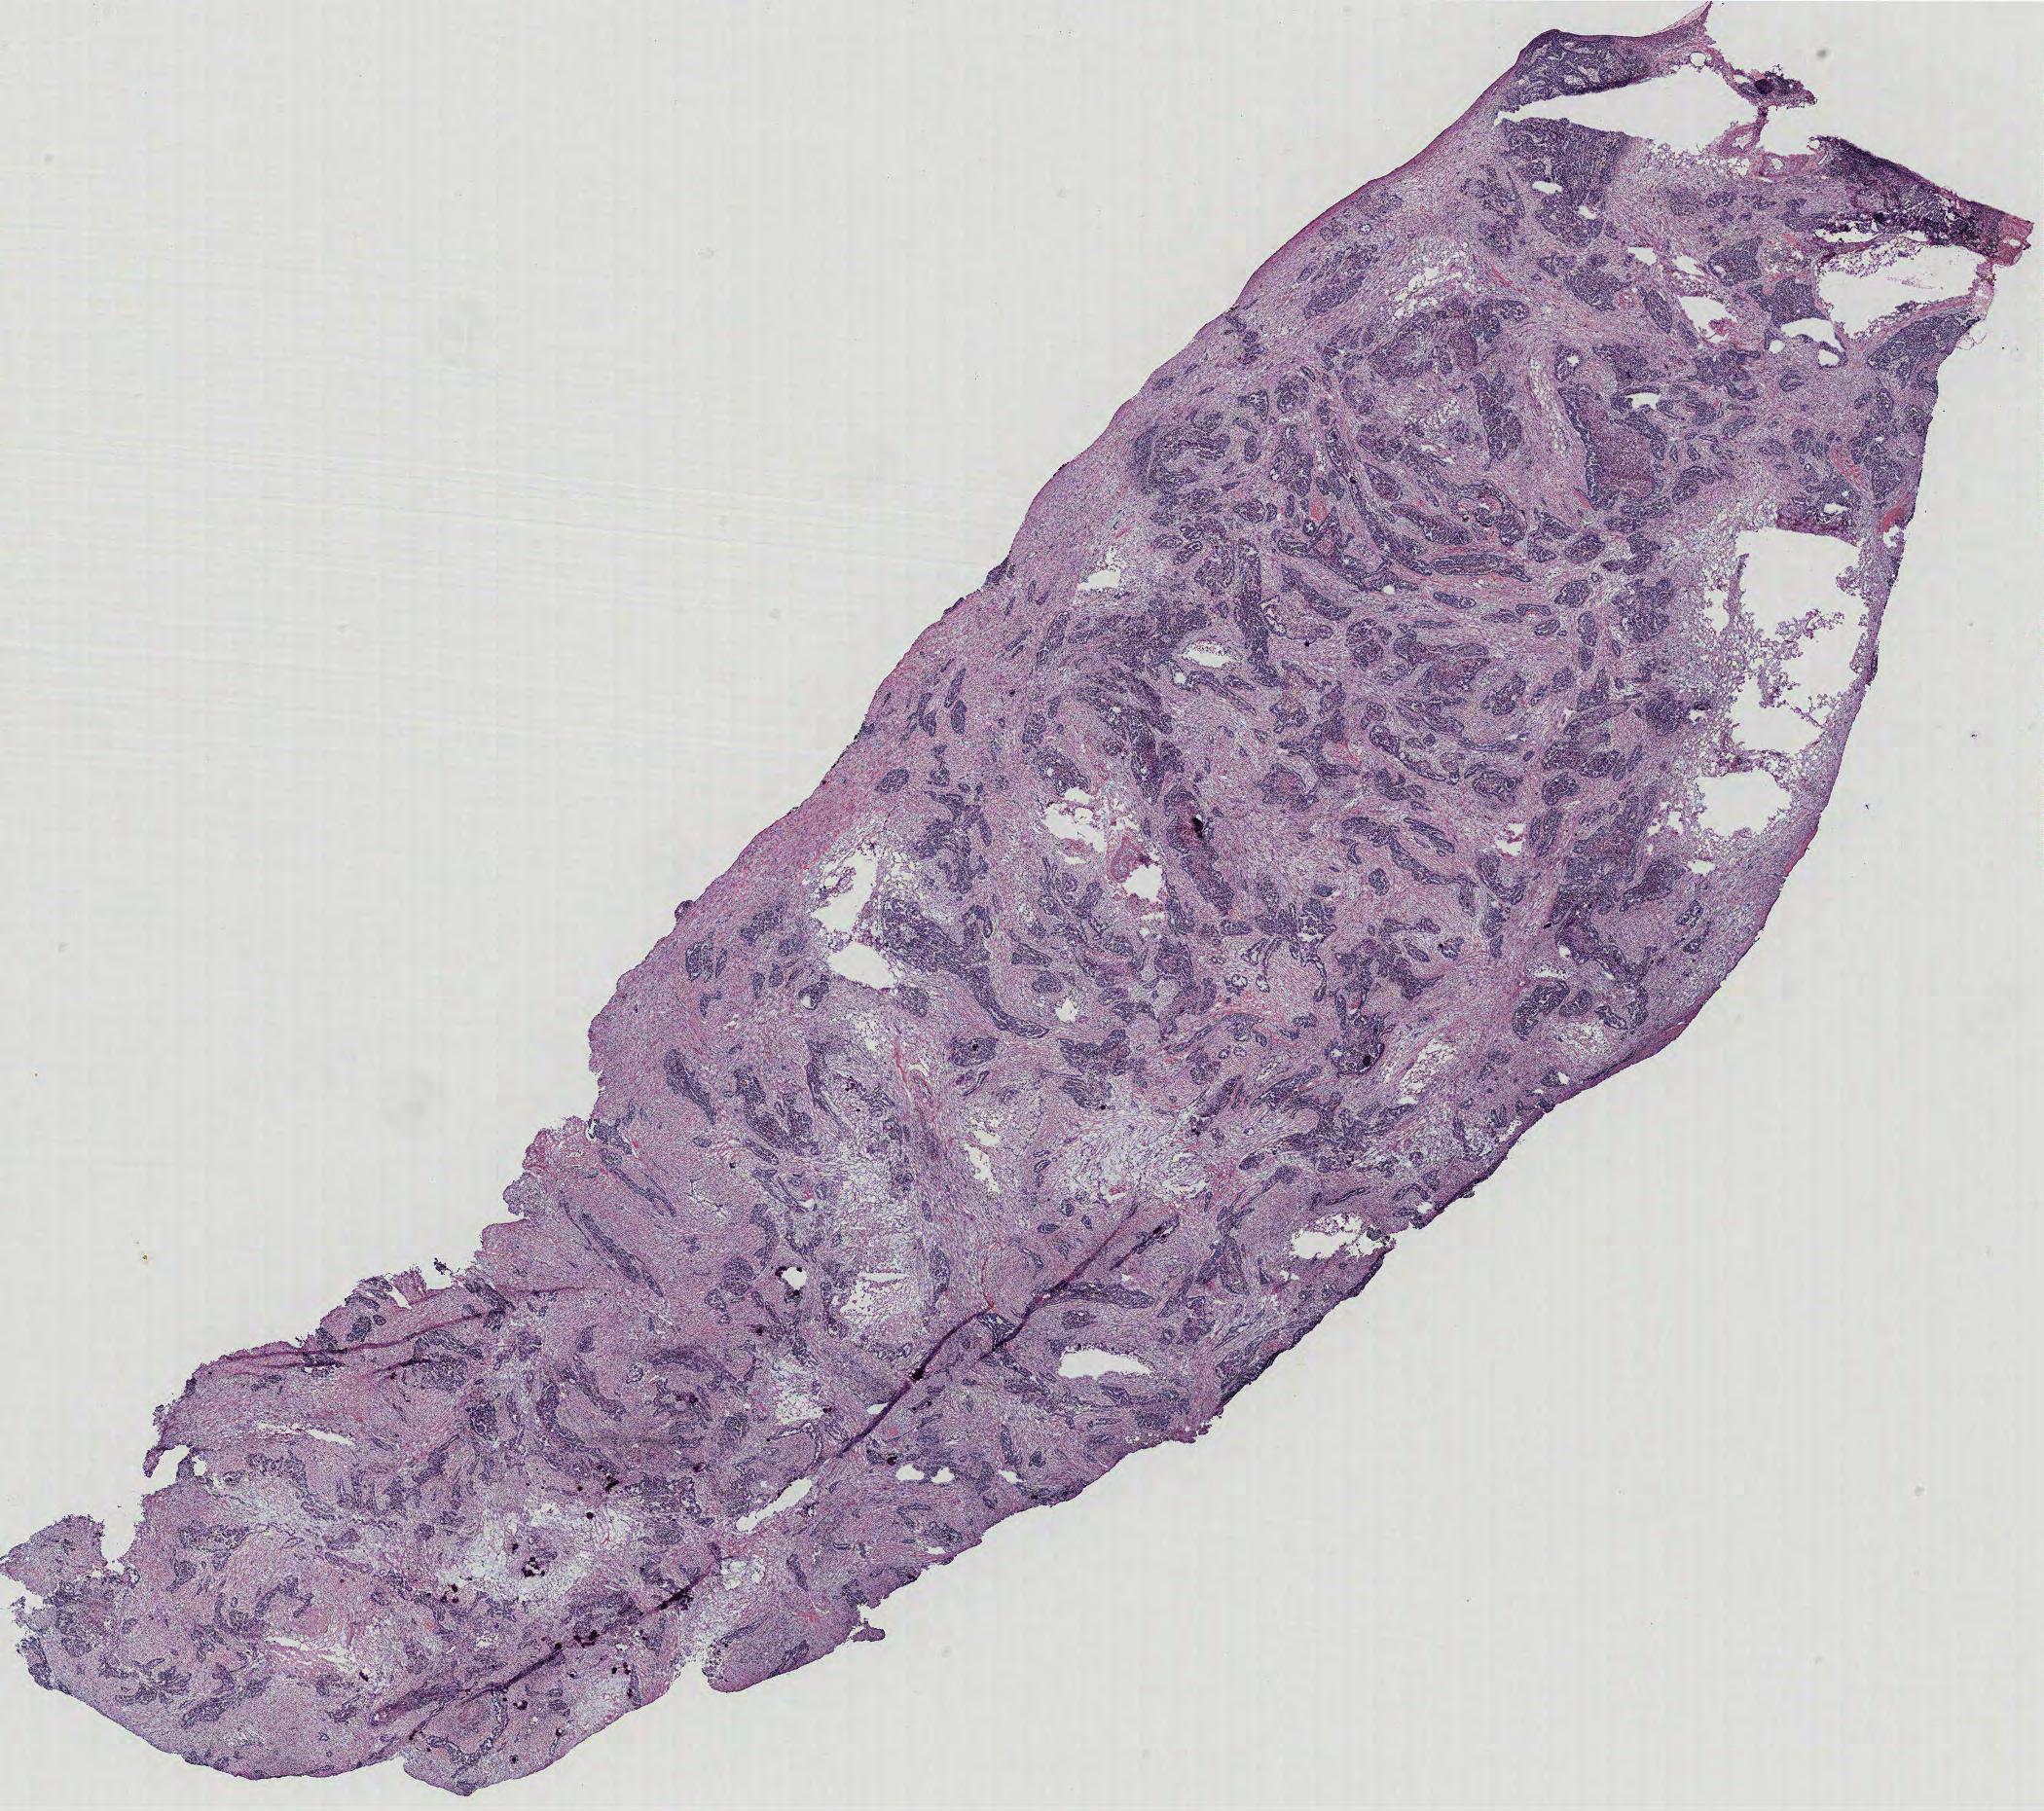
Hematoxylin and eosin (H&E) stained whole-slide image — whole scanned area (about 16.8 x 14.9 mm, slide scanned at 40x) shown as a low-resolution overview, ovary, tissue type not recorded. Female patient.
• patient diagnosis: Serous adenocarcinoma, NOS